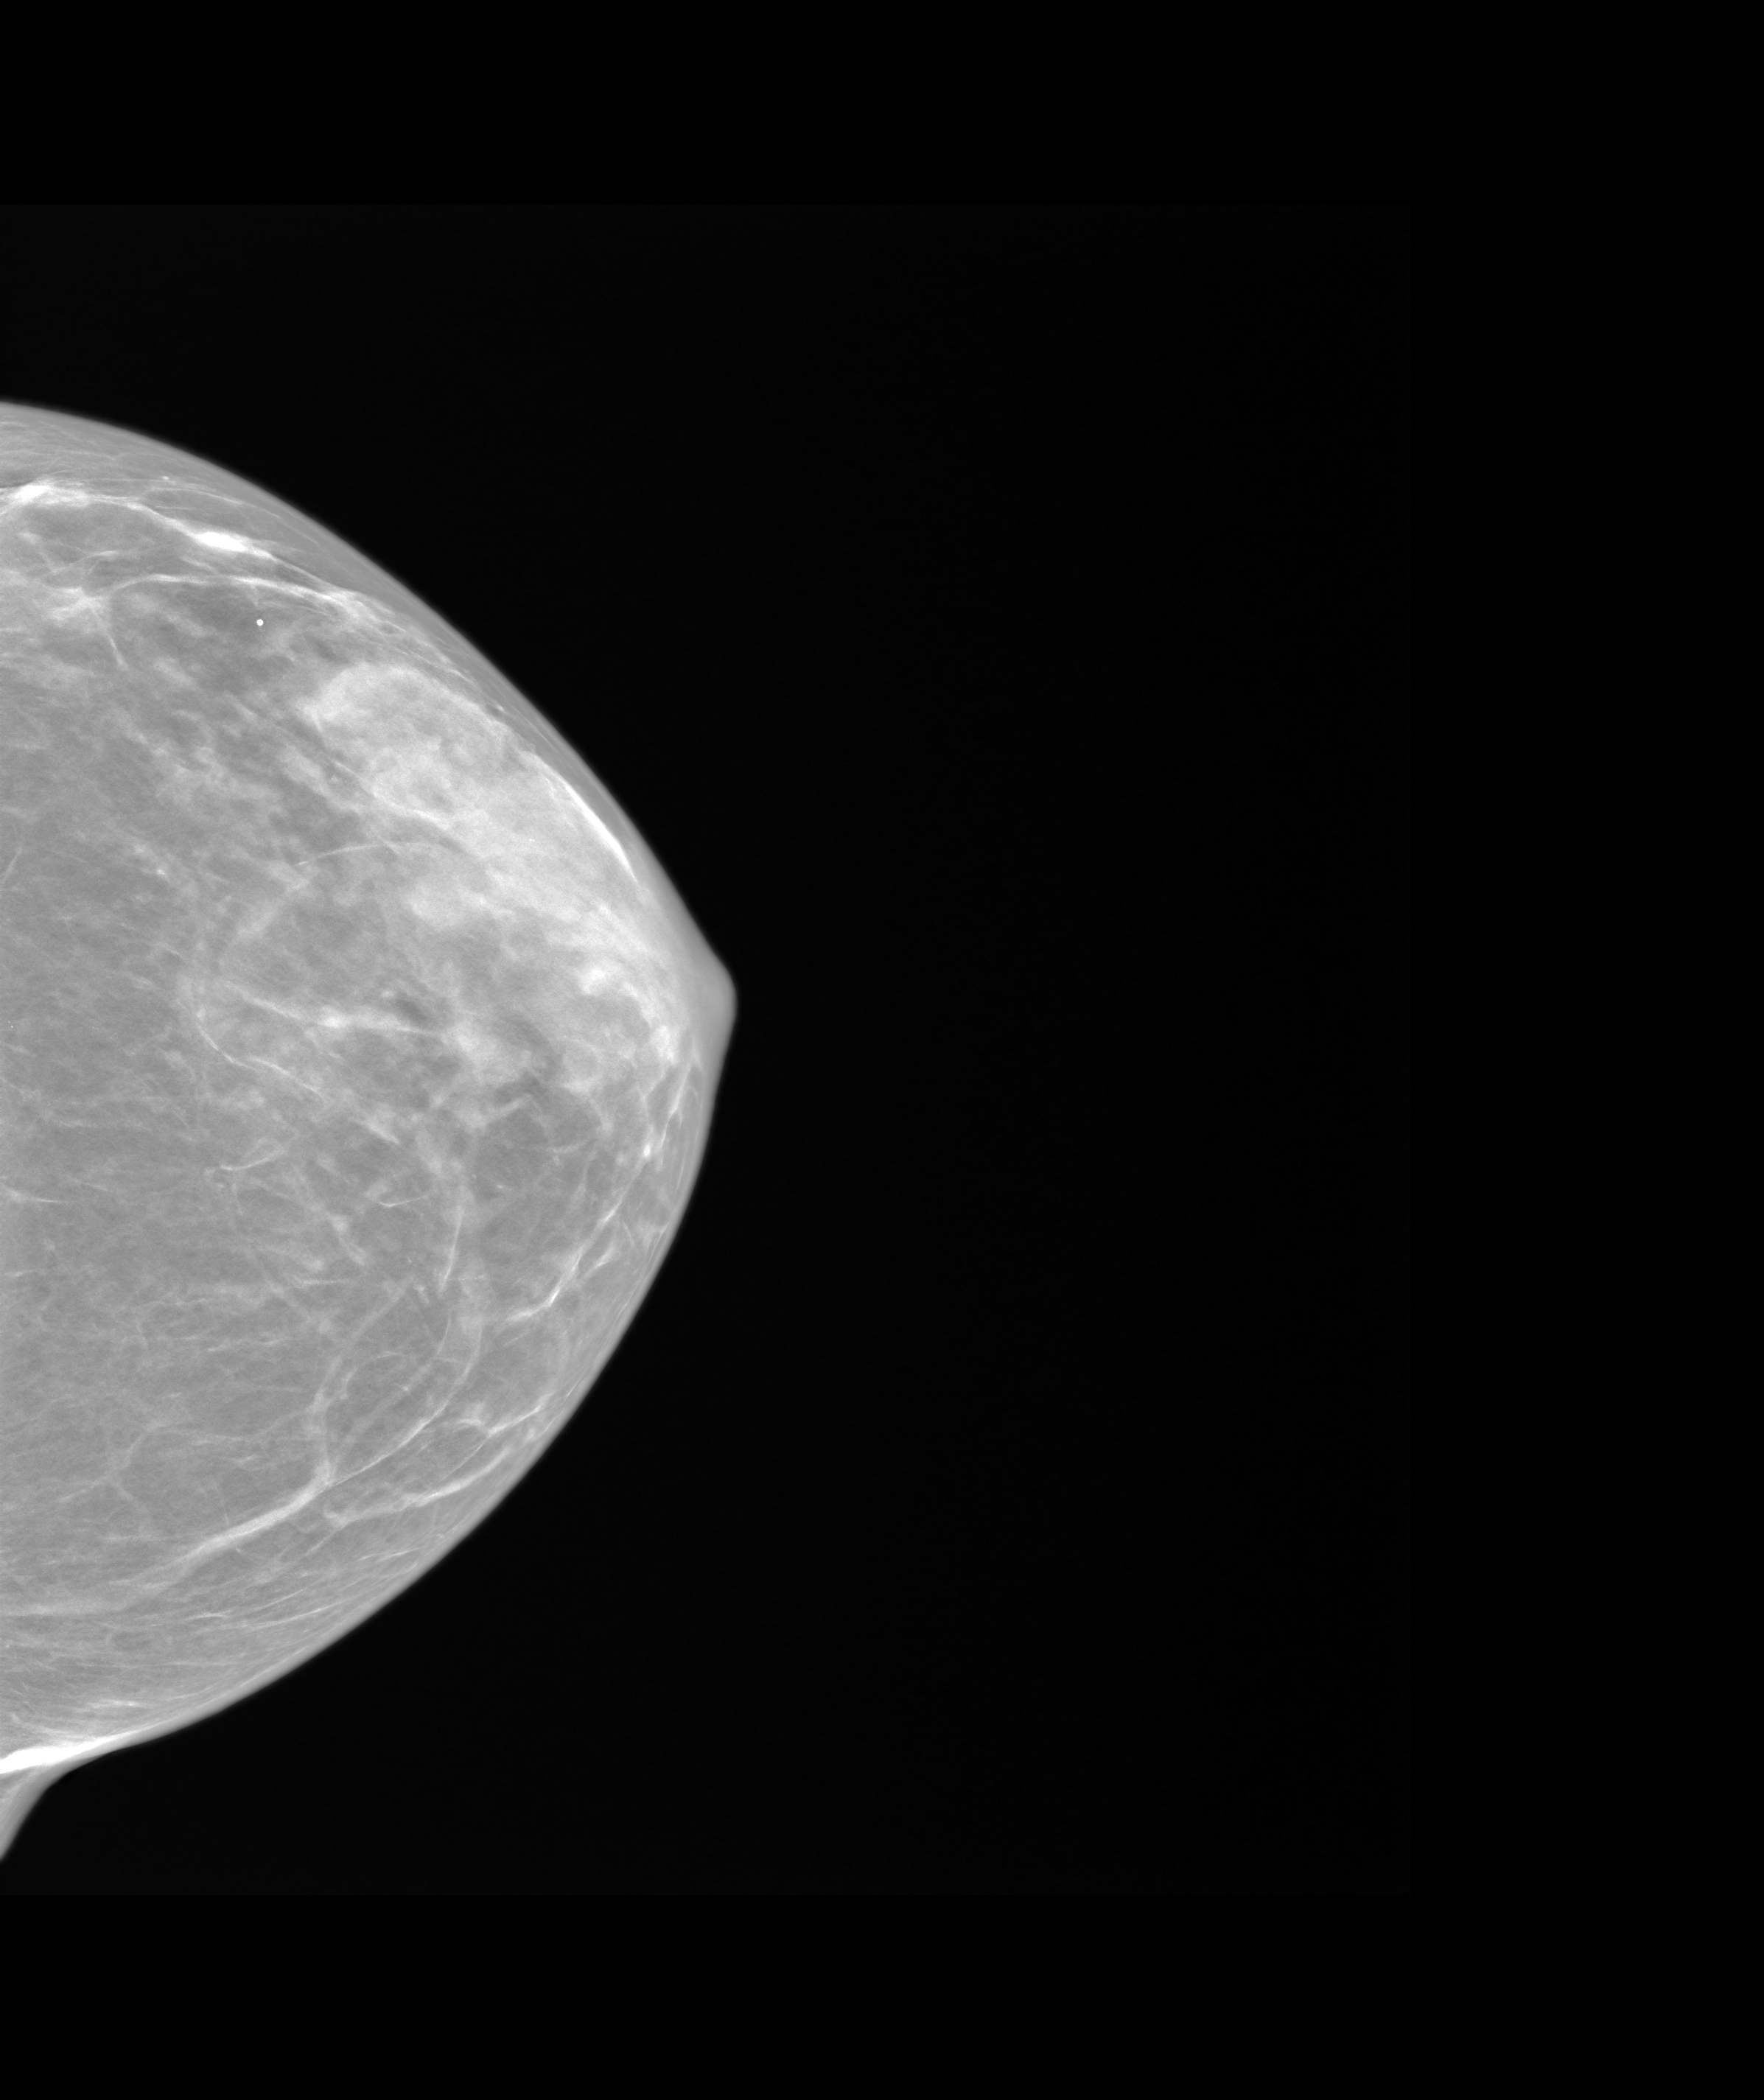
Annual screening mammography examination; system: SenoIris_1SP1.2(425). Patient: female, 43 years.
Image type: synthesized 2-D view from tomosynthesis. Breast: left. Projection: craniocaudal (CC) view. Breast density at the screening exam (both breasts): heterogeneously dense (BI-RADS density category c). Final BI-RADS assessment for this screening round (tomosynthesis exam, both breasts): category 1. Recall: no recall after this screen.